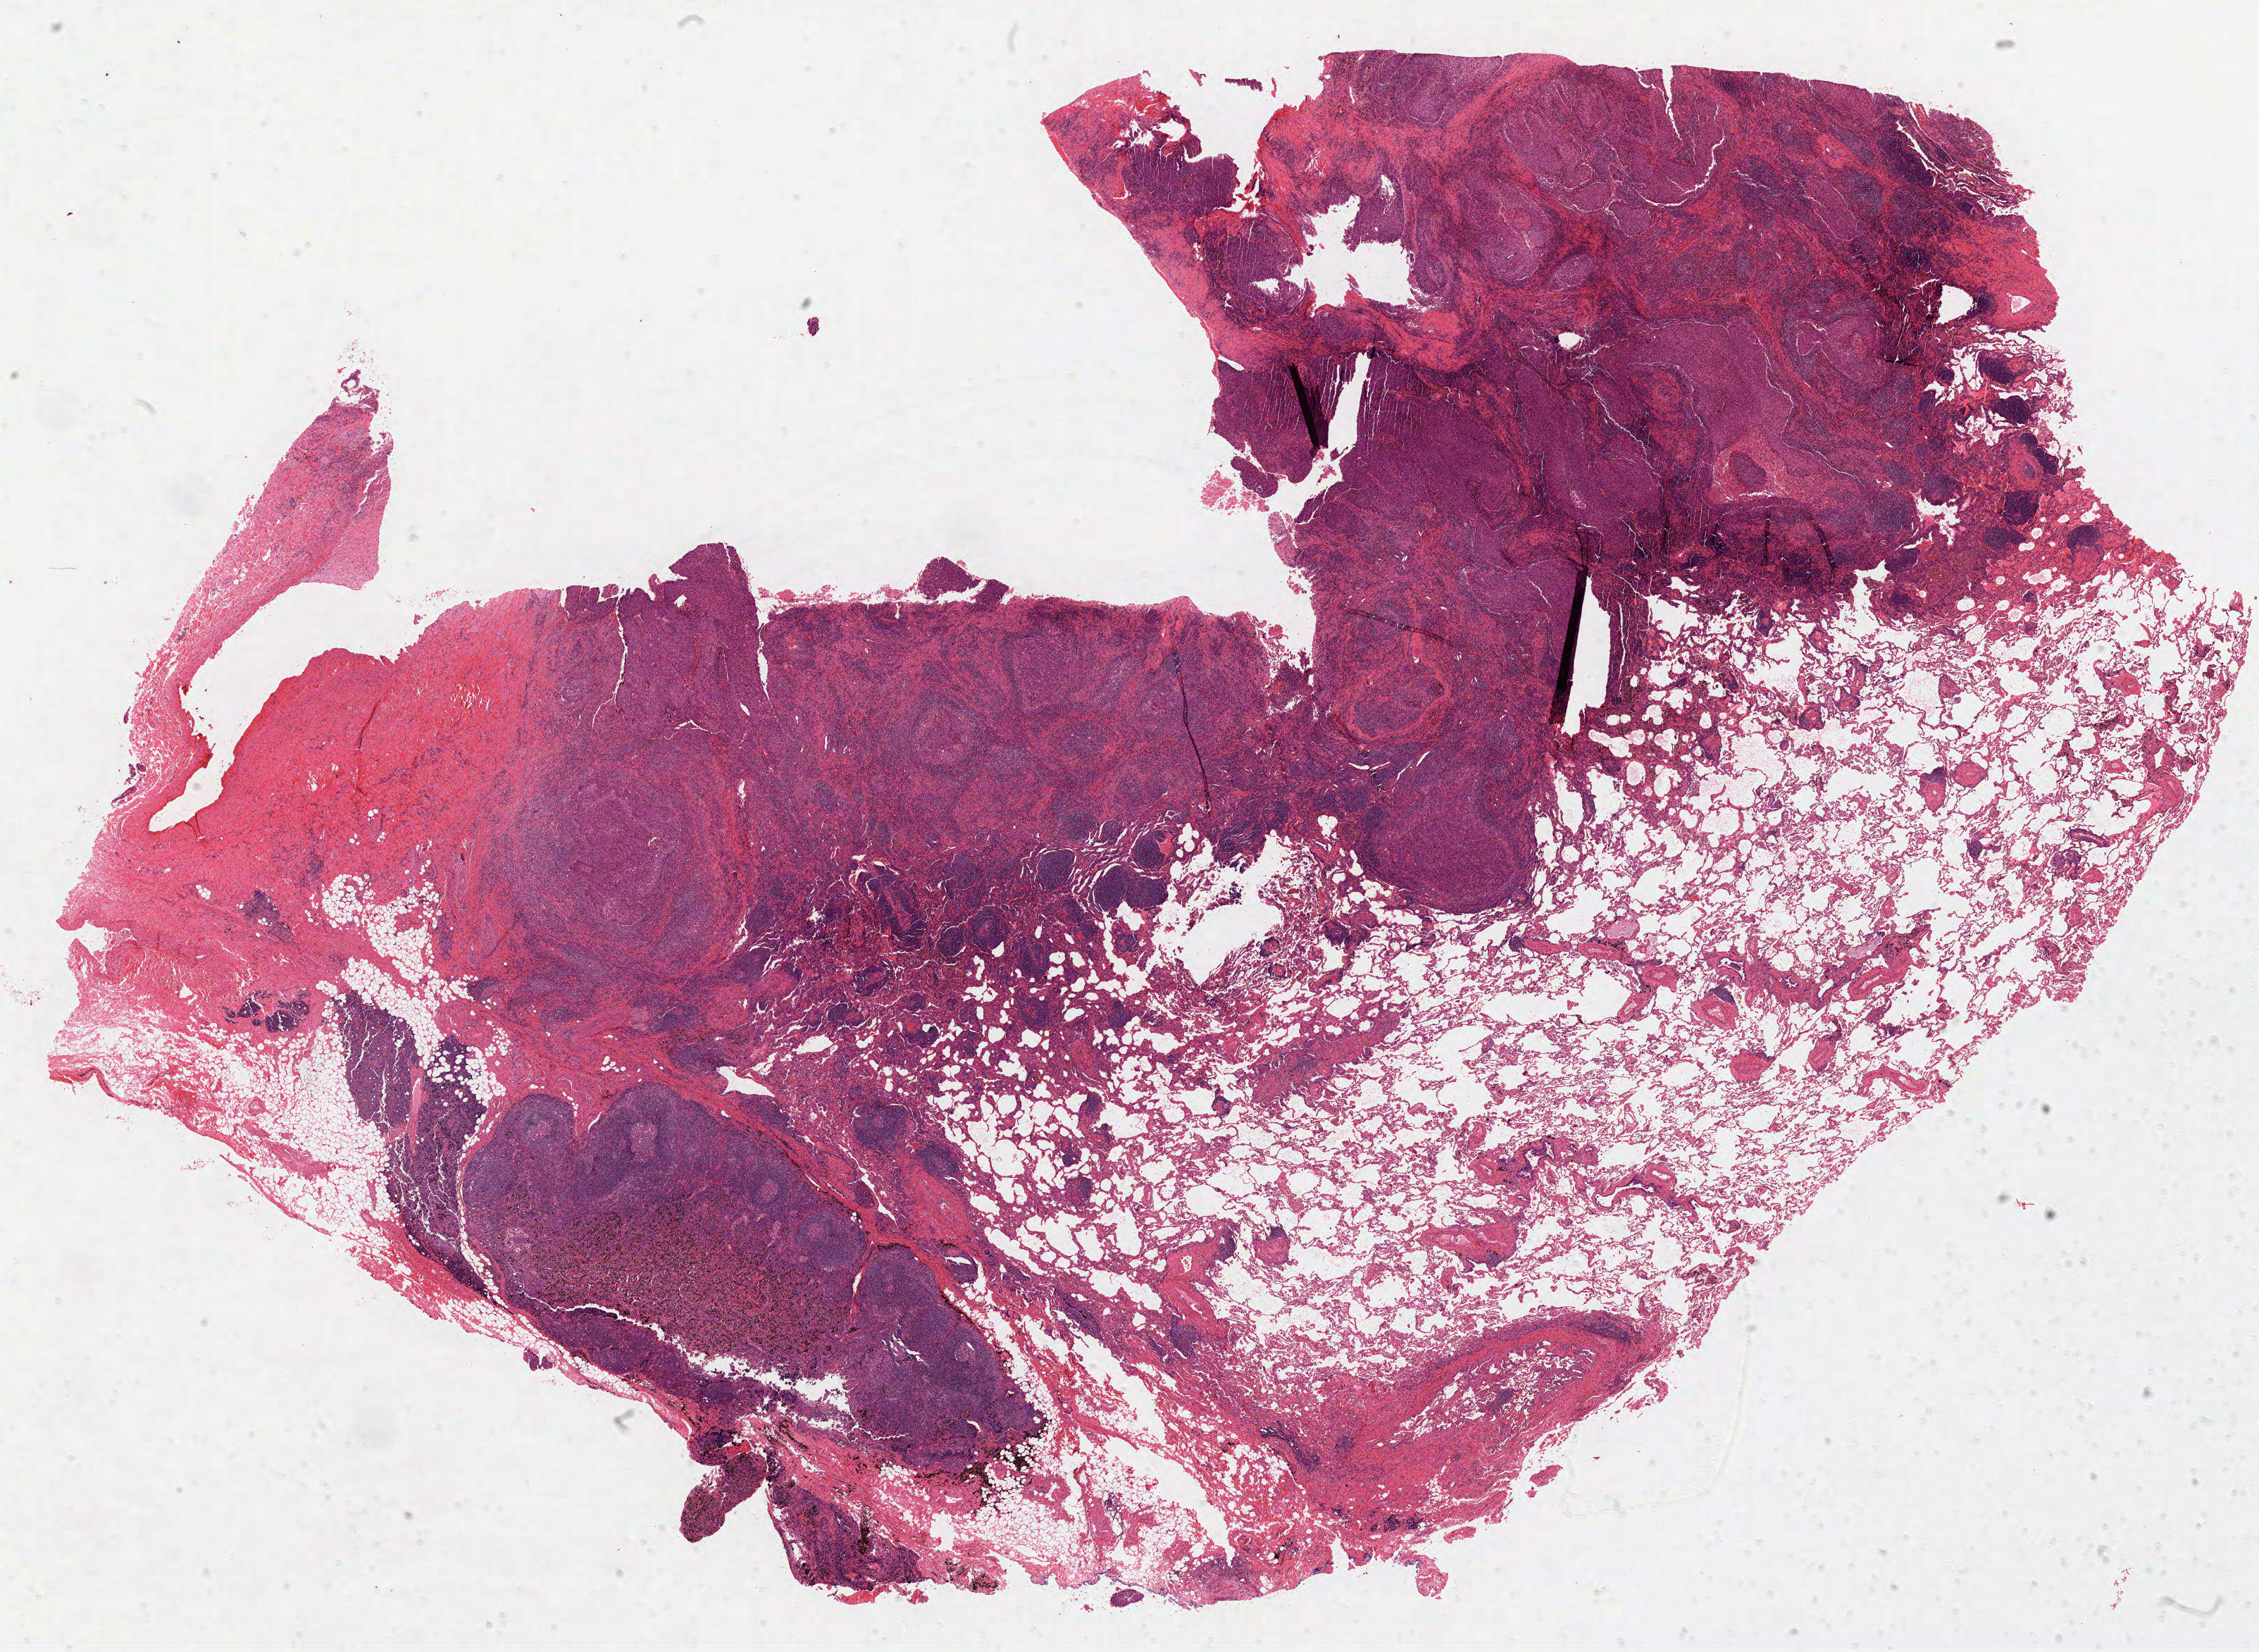
H&E whole-slide image — a low-resolution overview of the entire scanned area, about 25.9 x 18.9 mm; FFPE section; primary tumour sample from the lung. Patient: male, age at initial diagnosis 58 years.
Diagnosis: Squamous cell carcinoma, NOS (upper lobe, lung).